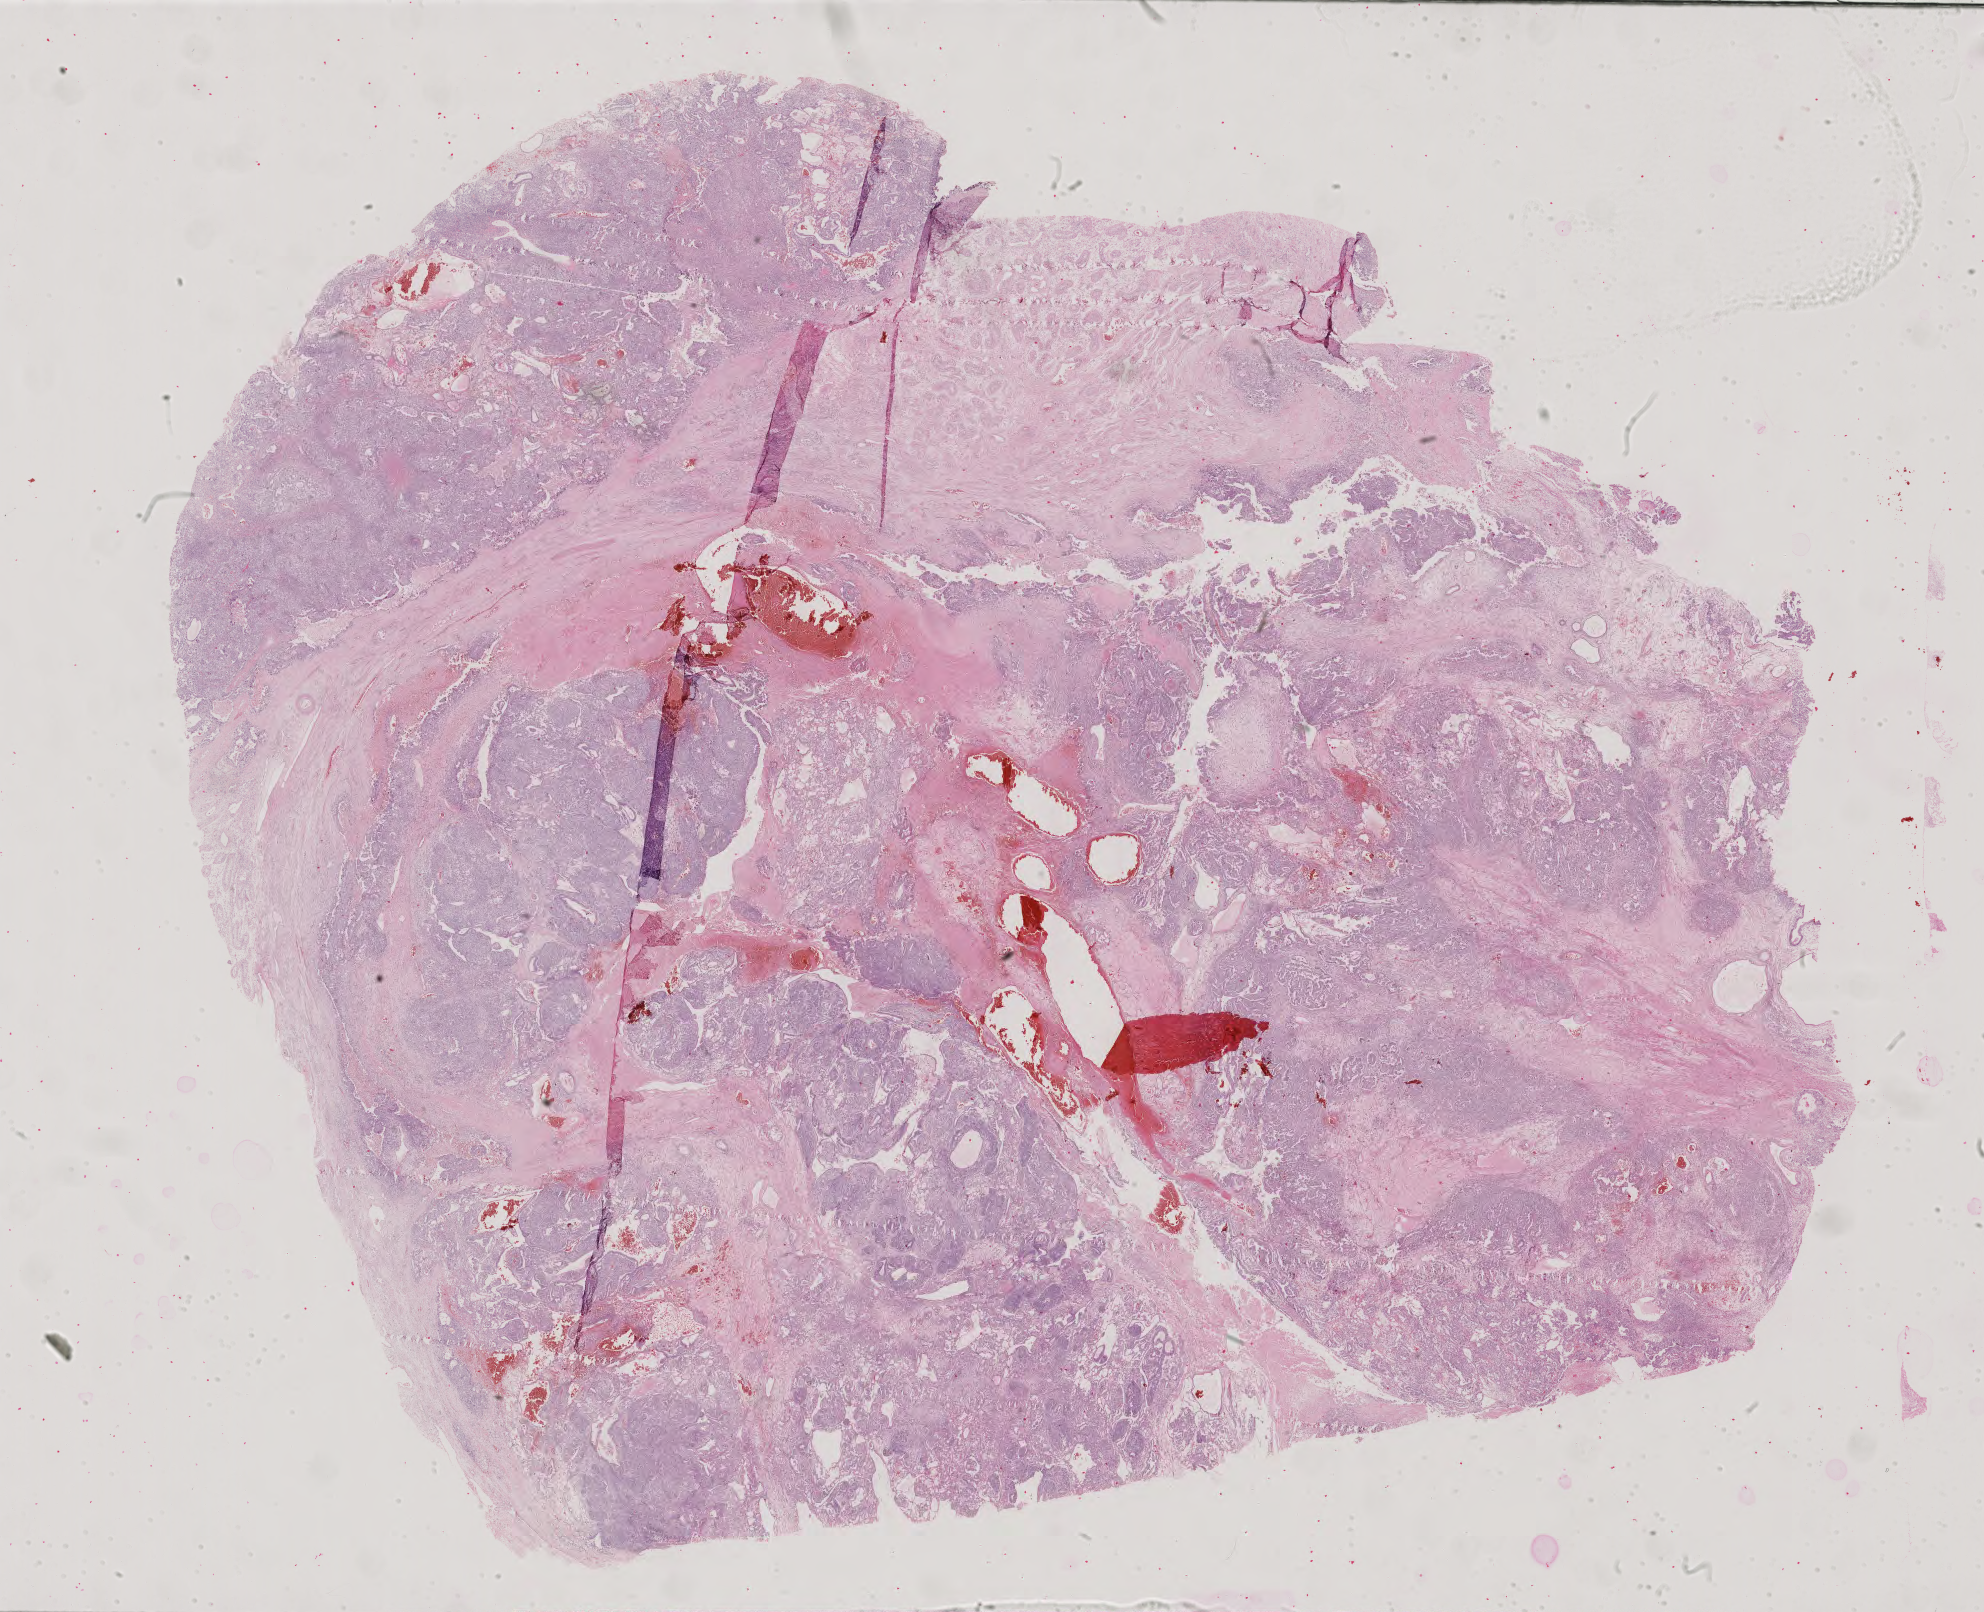
Digitized H&E tissue section (whole slide) — low-resolution overview of the scanned area, about 28.9 x 23.5 mm (acquisition: 40x scan), formalin-fixed paraffin-embedded (FFPE) diagnostic section, testis, primary tumour sample. Male, age 20 years at initial diagnosis.
- pathologic diagnosis: Mixed germ cell tumor
- AJCC pathologic stage: IS (6th edition)
- laterality: left